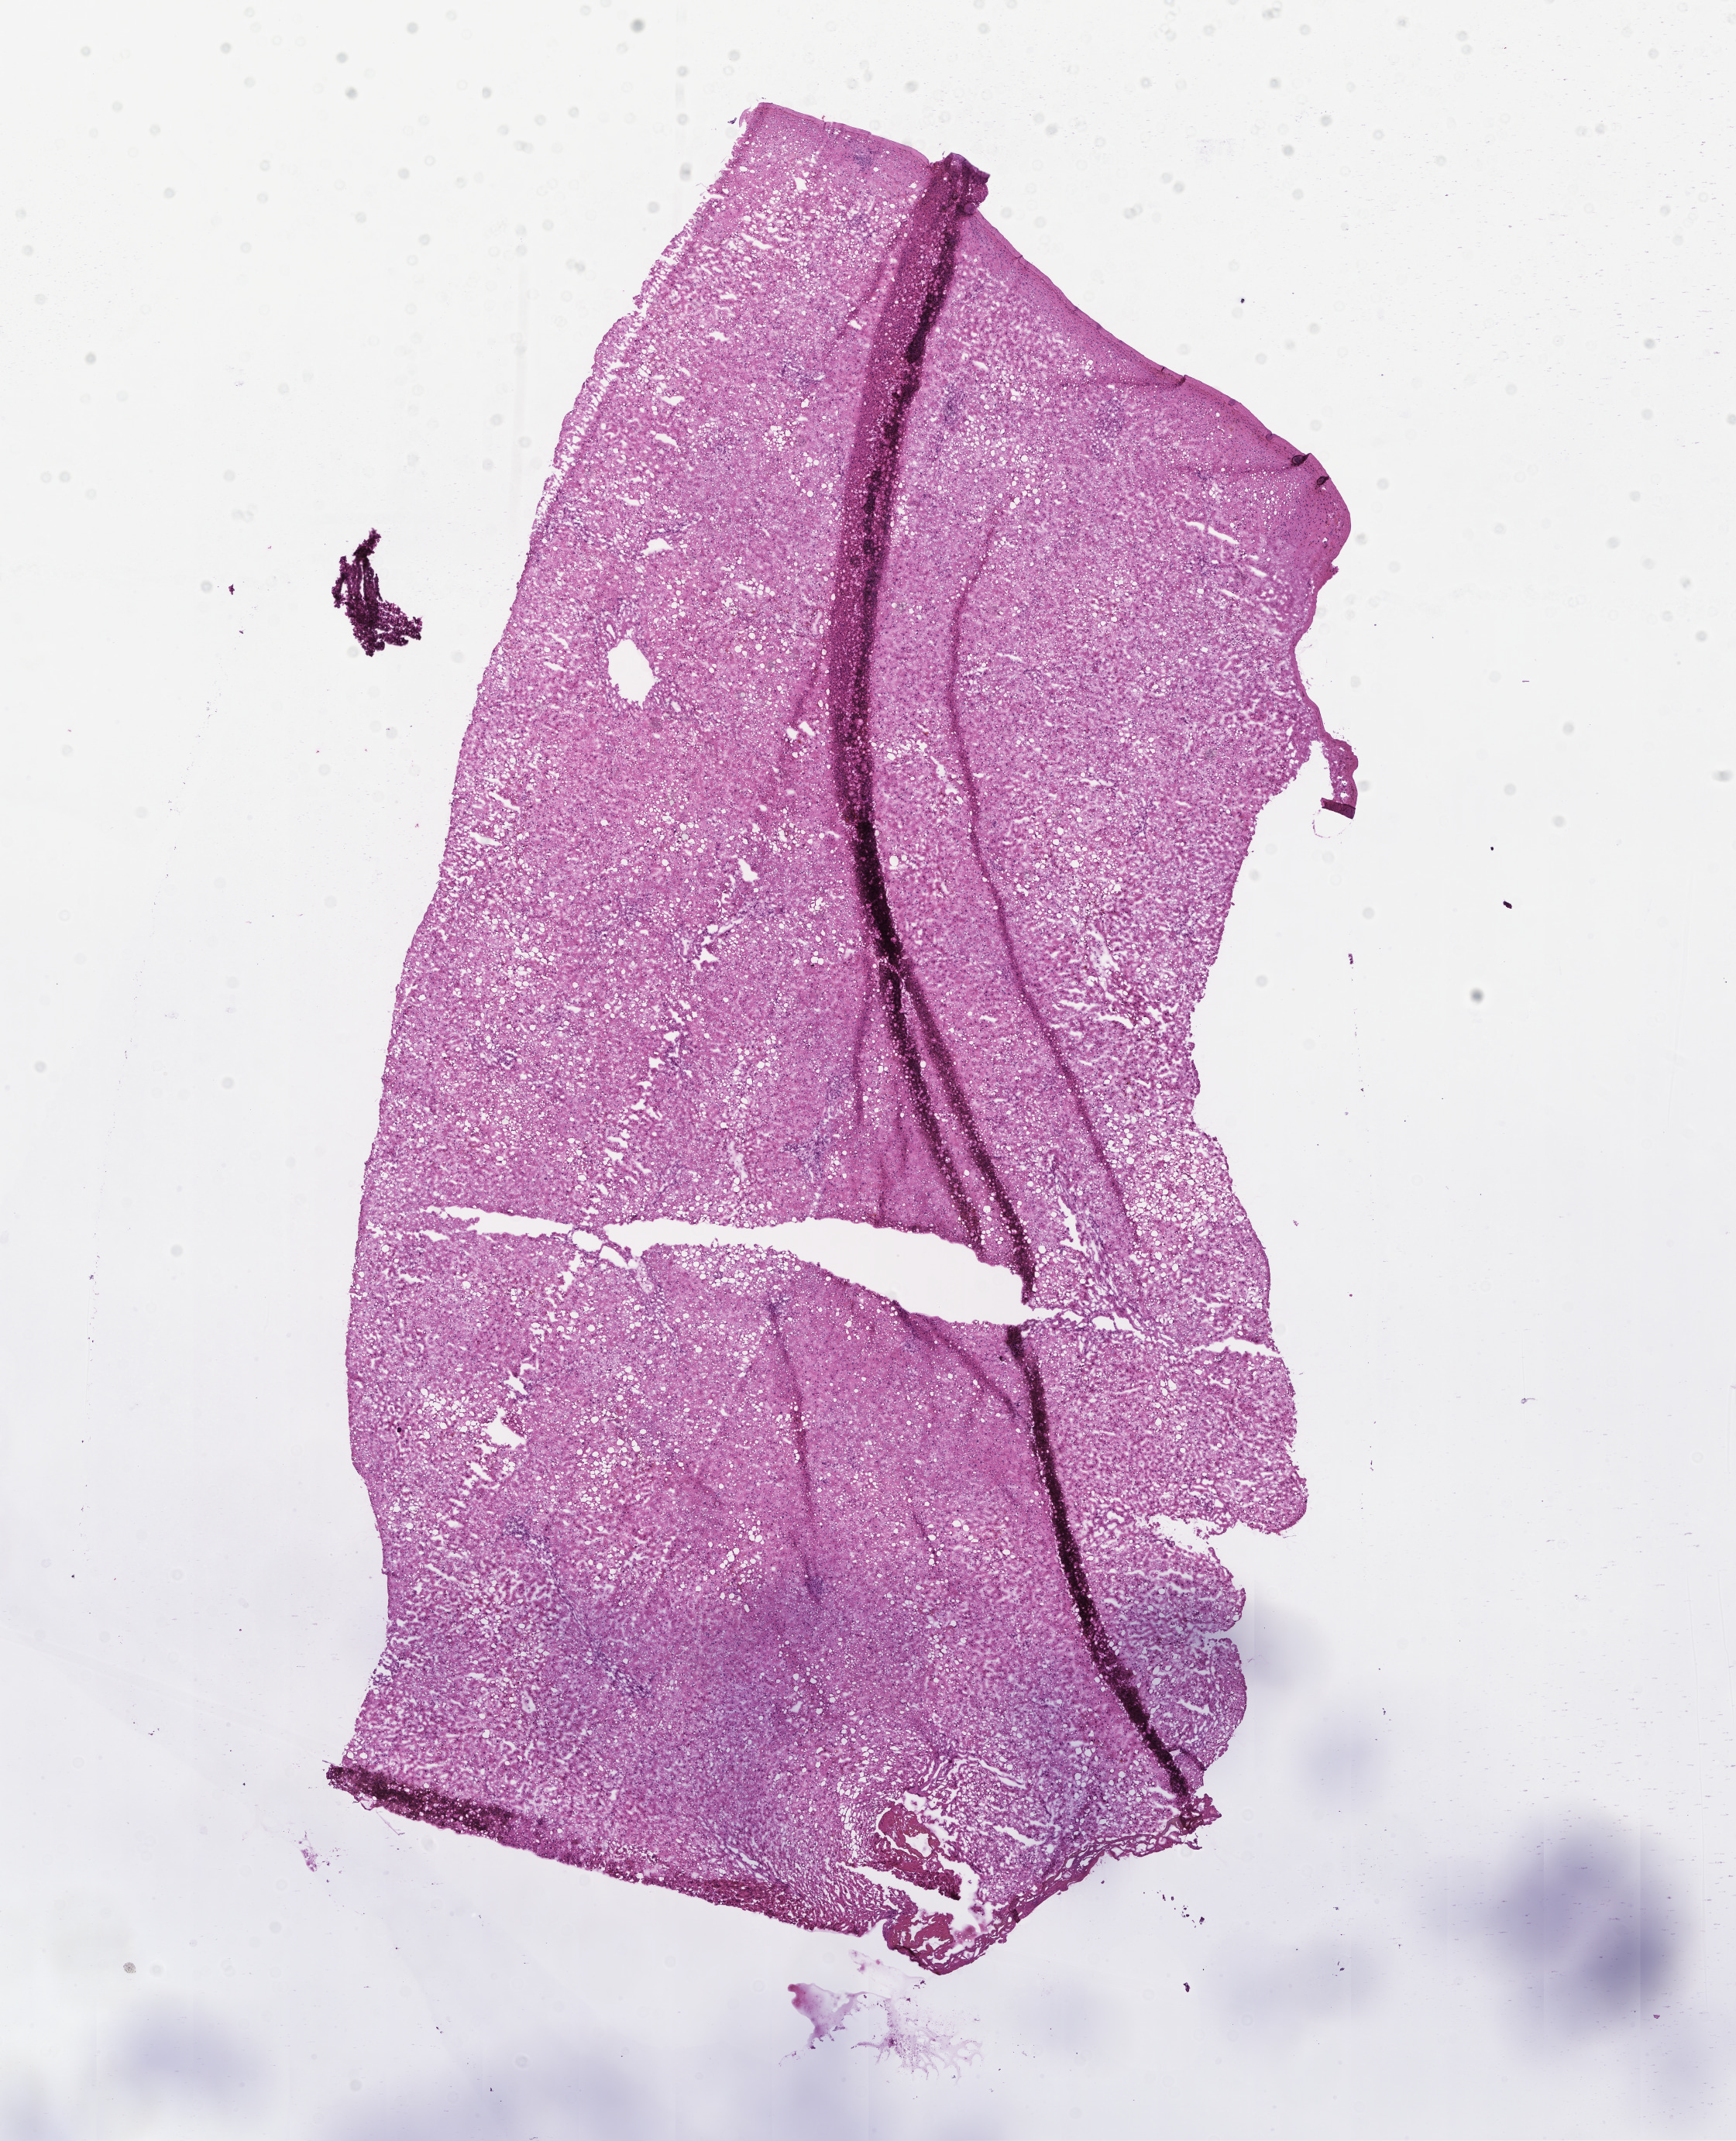
Whole-slide image, hematoxylin and eosin (H&E) stain — a low-resolution overview of the entire scanned area, about 9.1 x 11.2 mm, frozen section (tissue freezing medium), specimen: normal-tissue sample (non-tumor) from a patient with adenocarcinoma, NOS, site: colon. Patient: male, age at initial diagnosis 72 years. Pathologist review of this section (percent, as recorded): tumor cells 0%, tumor nuclei 0%, stromal cells 0%, necrosis 0%, normal cells 100%. Infiltration values recorded for this section: lymphocyte infiltration 5%, monocyte infiltration 0%, neutrophil infiltration 0%.
This section: non-tumor tissue sample; the patient's diagnosis is given above. Section: top of the tissue portion.